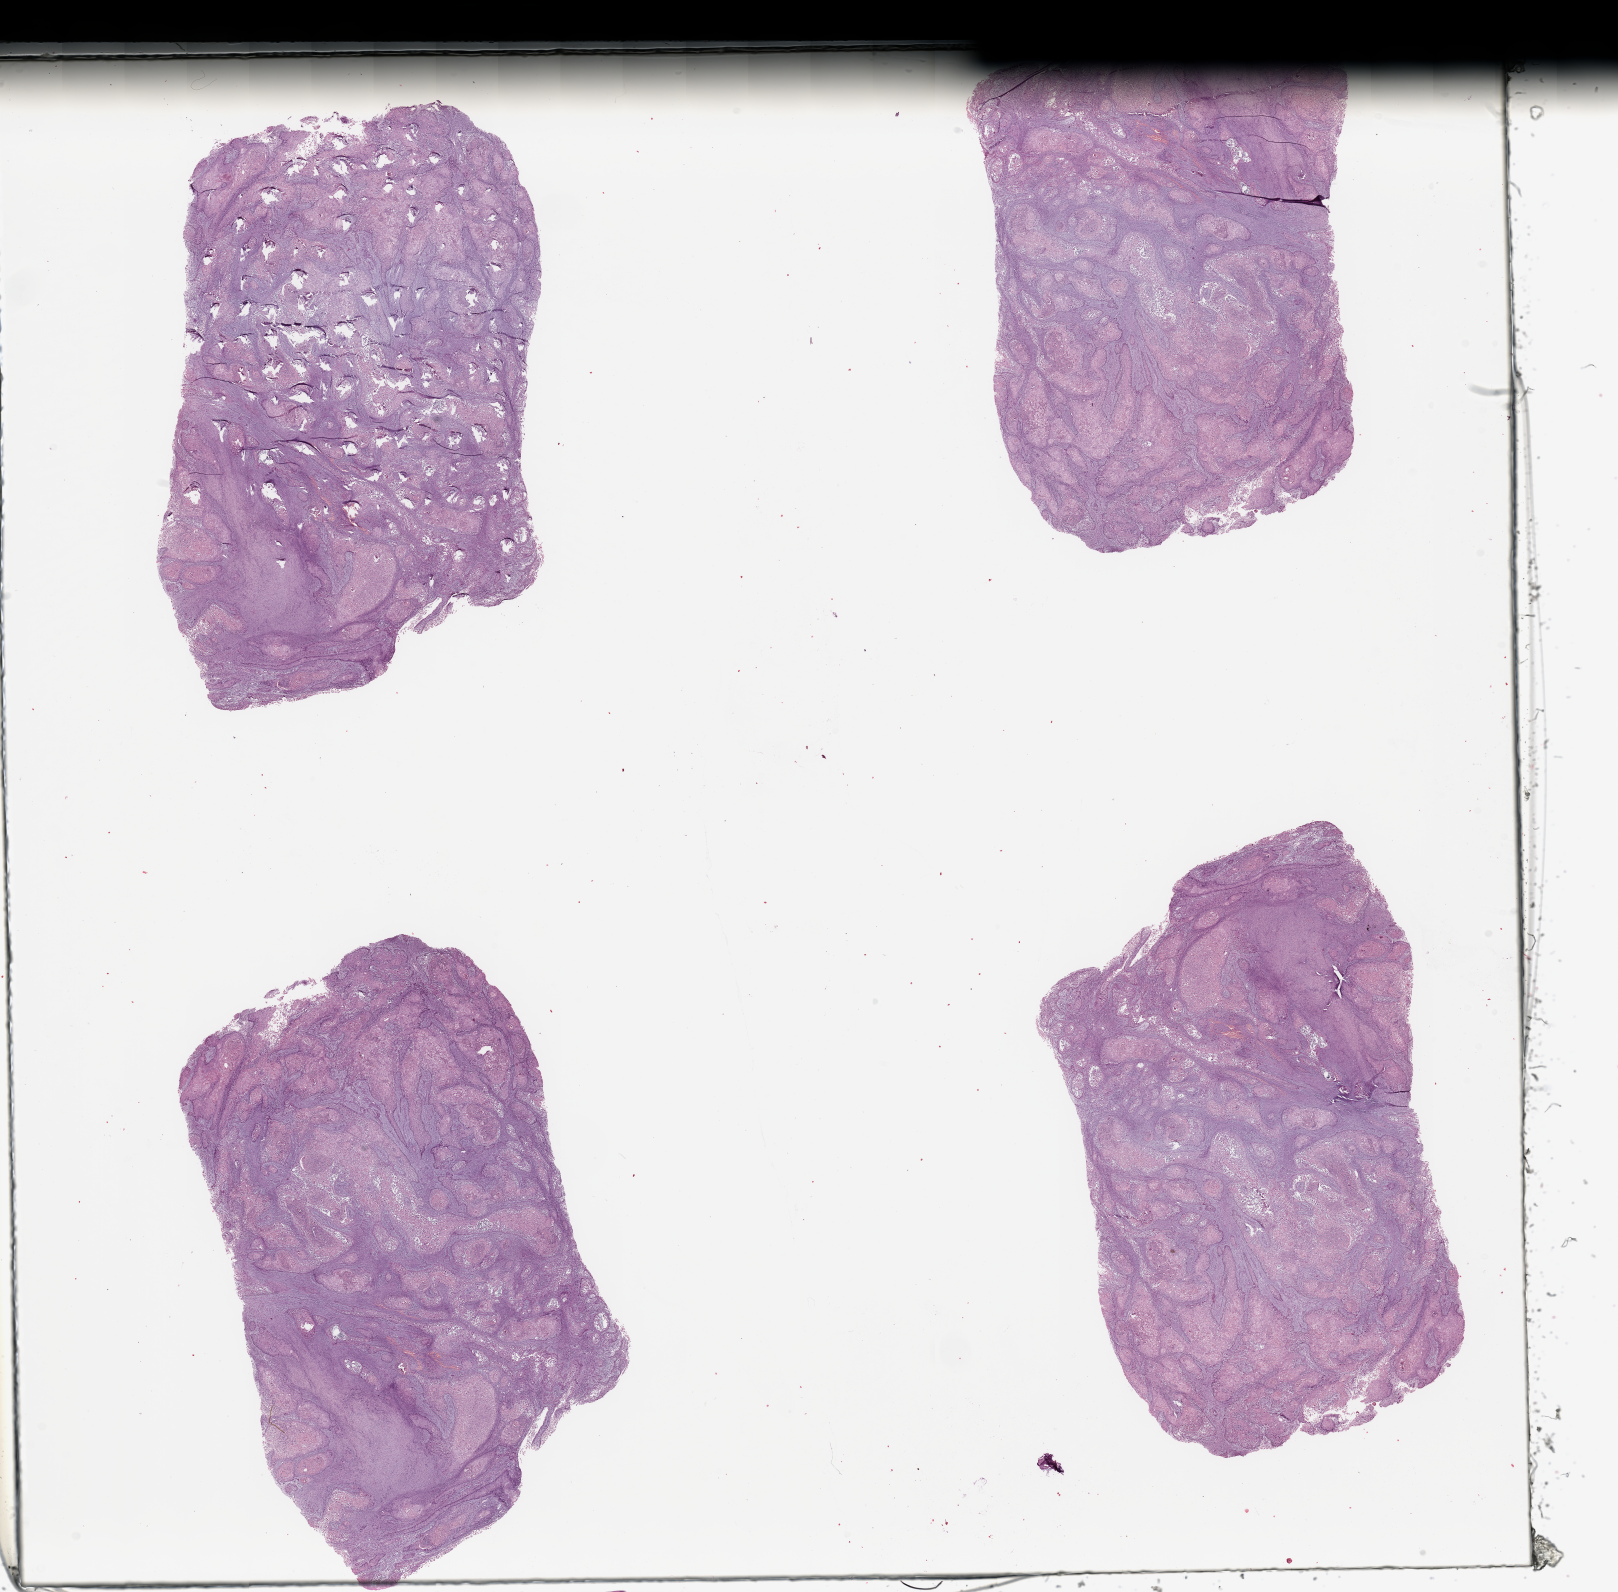
Whole-slide histology image, H&E, shown as a low-resolution overview of the whole scanned area (about 25.6 x 25.2 mm), head and neck, tissue type not recorded. Patient: male, age 53 years.
Patient diagnosis: Squamous cell carcinoma, NOS (gum, NOS).